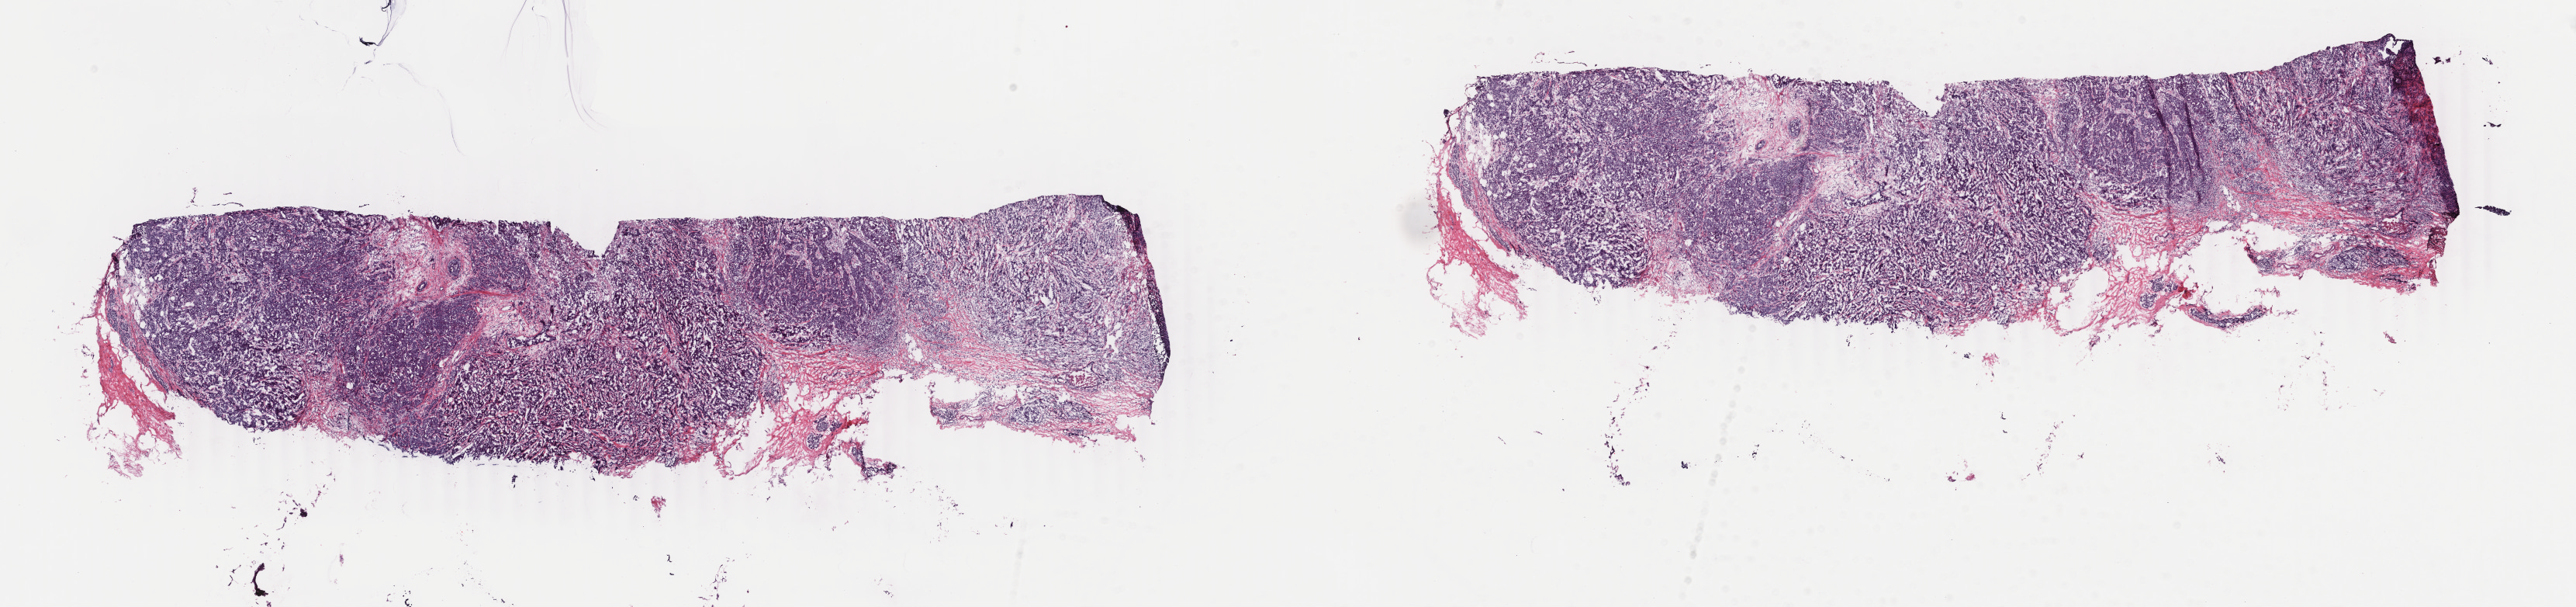
Whole-slide histology image, Hematoxylin and eosin (H&E) stained, low-resolution overview of the scanned area, about 26.4 x 6.2 mm (from a 40x scan), frozen section, sample: primary tumour, breast. Female, age 59 years at initial diagnosis. Composition of this section per pathologist review: tumour cells 93%, tumour nuclei 85%, normal cells 2%, stromal cells 5%, necrosis 0%. Inflammatory infiltration, as recorded: lymphocyte infiltration 0%, monocyte infiltration 0%, neutrophil infiltration 0%.
Diagnosis: Infiltrating duct carcinoma, NOS. AJCC pathologic stage: IIB (6th edition).